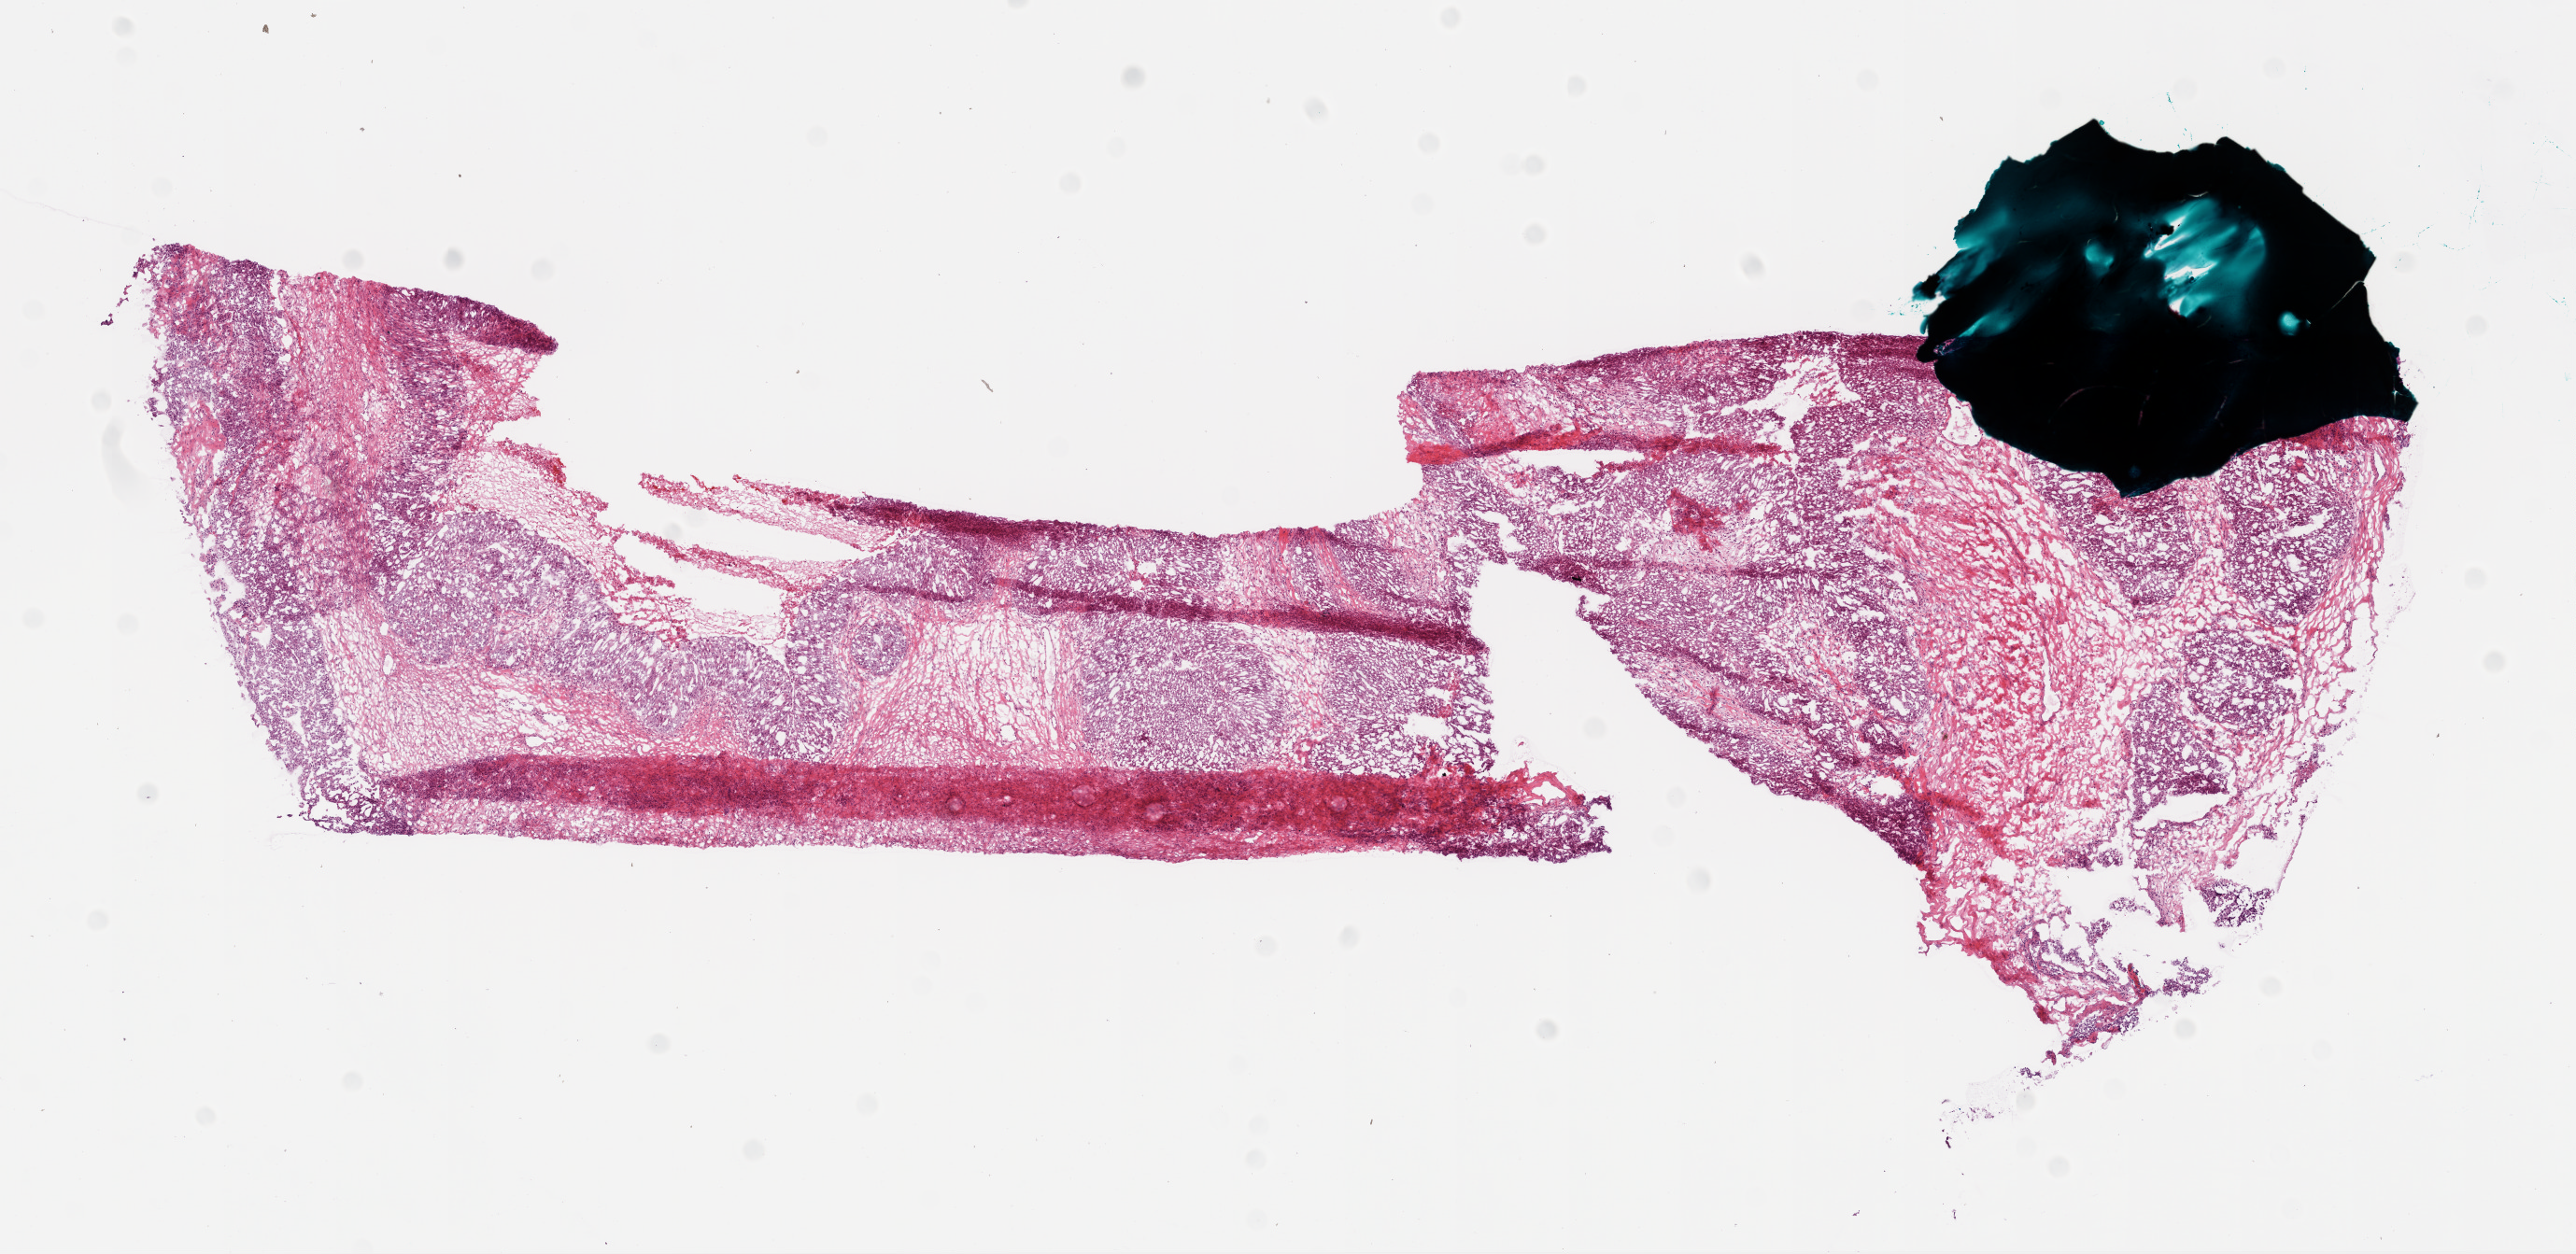
Digitized H&E tissue section (whole slide) — whole scanned area (about 11.1 x 5.4 mm, from a 20x scan) shown as a low-resolution overview; frozen section from the bottom of the tissue portion; ovary, primary tumour sample. Patient: female, age at initial diagnosis 43 years. Histologic grade: G3 (poorly differentiated). Composition of this section per pathologist review: tumour cells 70%, tumour nuclei 75%, normal cells 15%, stromal cells 10%, necrosis 5%.
* diagnosis: Serous cystadenocarcinoma, NOS
* FIGO stage: IIIC